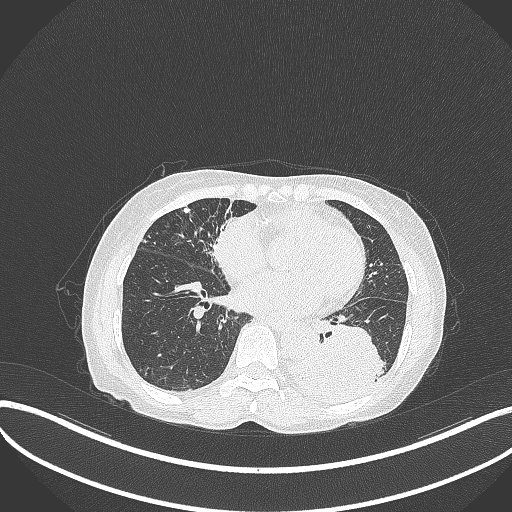
Chest CT, one axial slice; reconstruction kernel B70f; 120 kVp; lung window (W 1500 / L -600 HU); 1 mm slice thickness; 512 × 512 image matrix. Female patient, age 78 years. From the clinical record (not read from this slice): clinical TNM (as recorded): T3 N0 M1.
Structures marked on this image (rectangle marked by the reading radiologist):
- lung tumour (recorded histology: squamous cell carcinoma): bounding box [x1, y1, x2, y2] px = [290, 318, 386, 396]